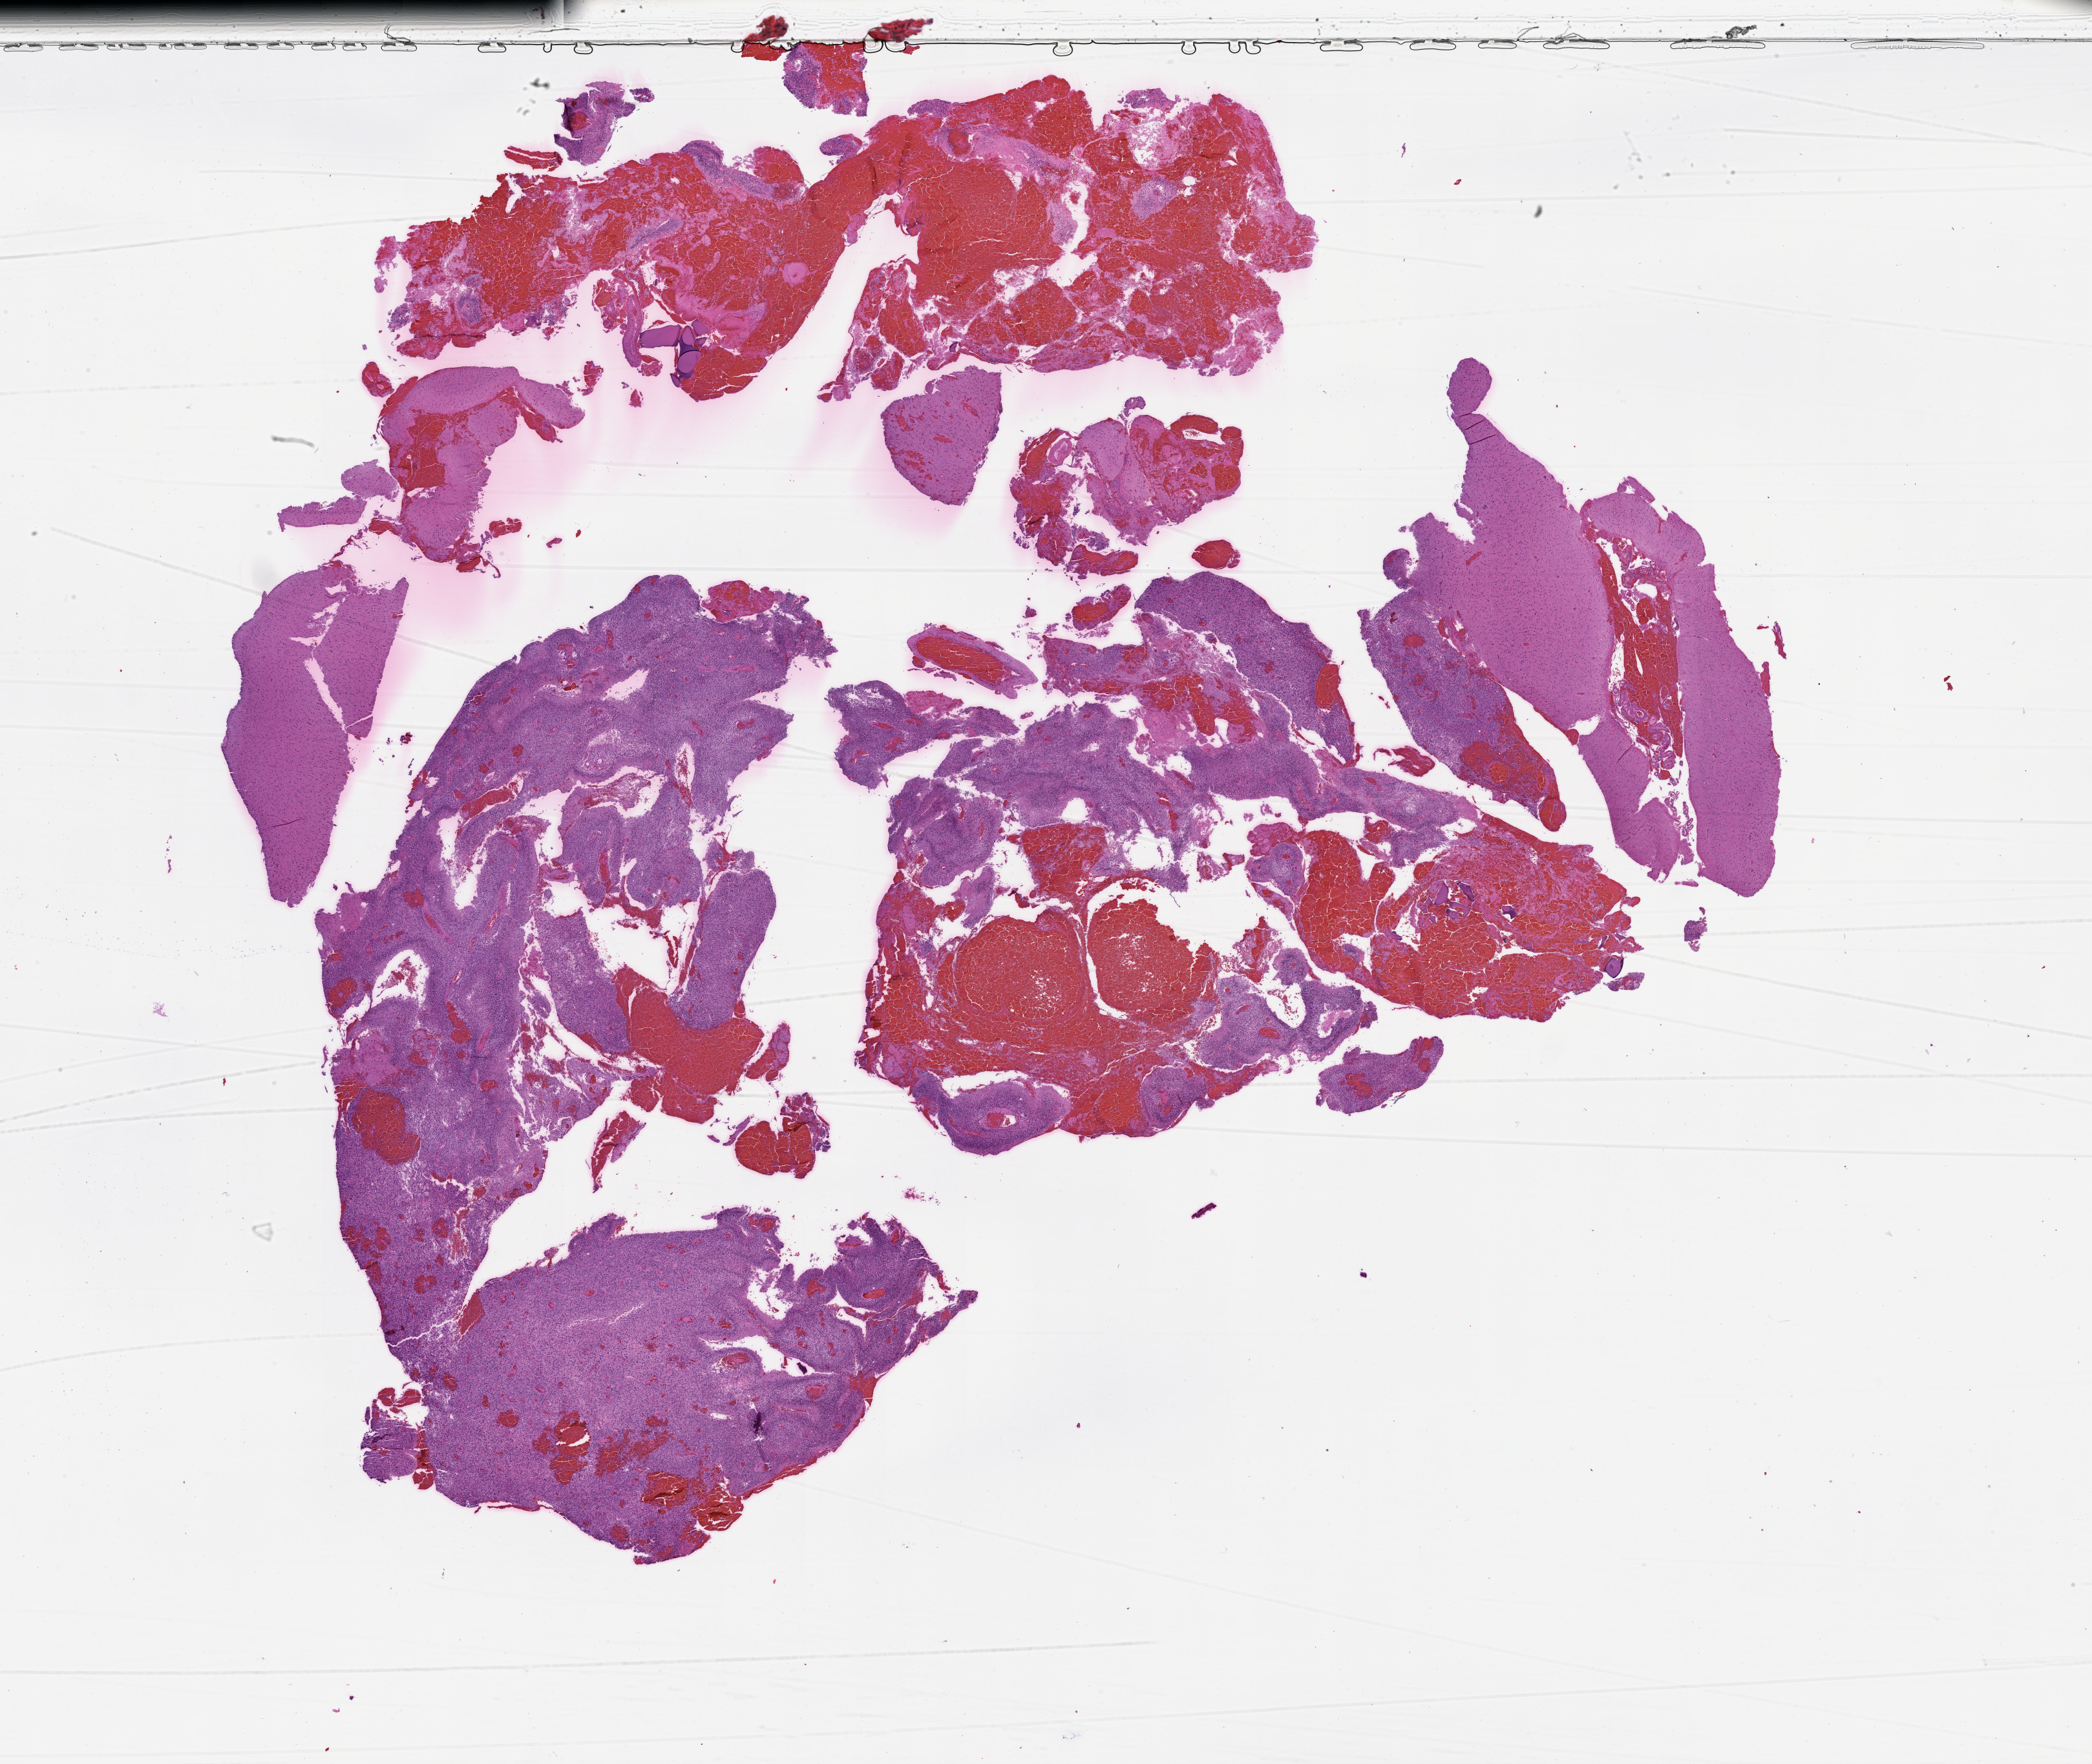
Digitized Hematoxylin and eosin (H&E) stained tissue section (whole slide), whole scanned area (about 26.1 x 22.0 mm, slide scanned at 20x) shown as a low-resolution overview; tumour tissue sample, sampled site: brain. Patient: female, age 69 years. Pathologist review of this section (percent, as recorded): tumour nuclei 70%, necrosis 7%.
Diagnosis: Glioblastoma. Primary tumour site (as recorded): parietal lobe.